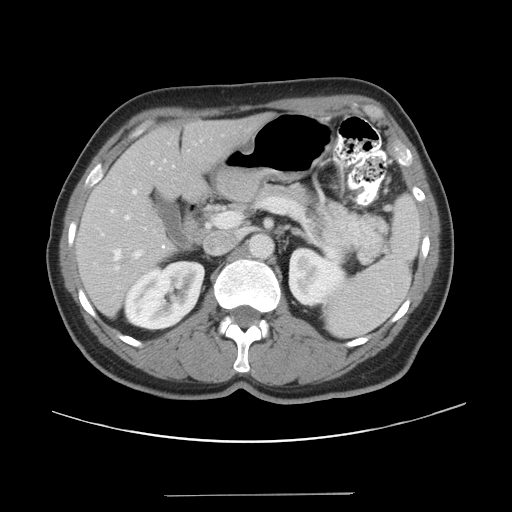
Contrast-enhanced abdominal CT, one axial slice; slice 21 of 43 in the series (ordered by position); reconstruction kernel STANDARD; 120 kVp; soft-tissue window (W 400 / L 40 HU); 5 mm slice thickness; 512 × 512 image matrix, field of view 409 × 409 mm. Male patient, age 65 years. Case-level facts recorded for this patient, not image findings: diagnosis: colorectal cancer liver metastases, imaged before liver resection; multiple liver metastases: no; largest metastasis: 3.8 cm; chemotherapy before resection: yes.
Annotated regions visible in this slice (expert manual segmentation):
- hepatic veins: bounding box (x1, y1, x2, y2) in pixels: (109, 188, 138, 260)
- liver: (77, 117, 264, 315)
- planned liver remnant (the part of the liver to remain after resection): (77, 116, 265, 315)
- portal vein (with intrahepatic branches): (101, 161, 154, 259)